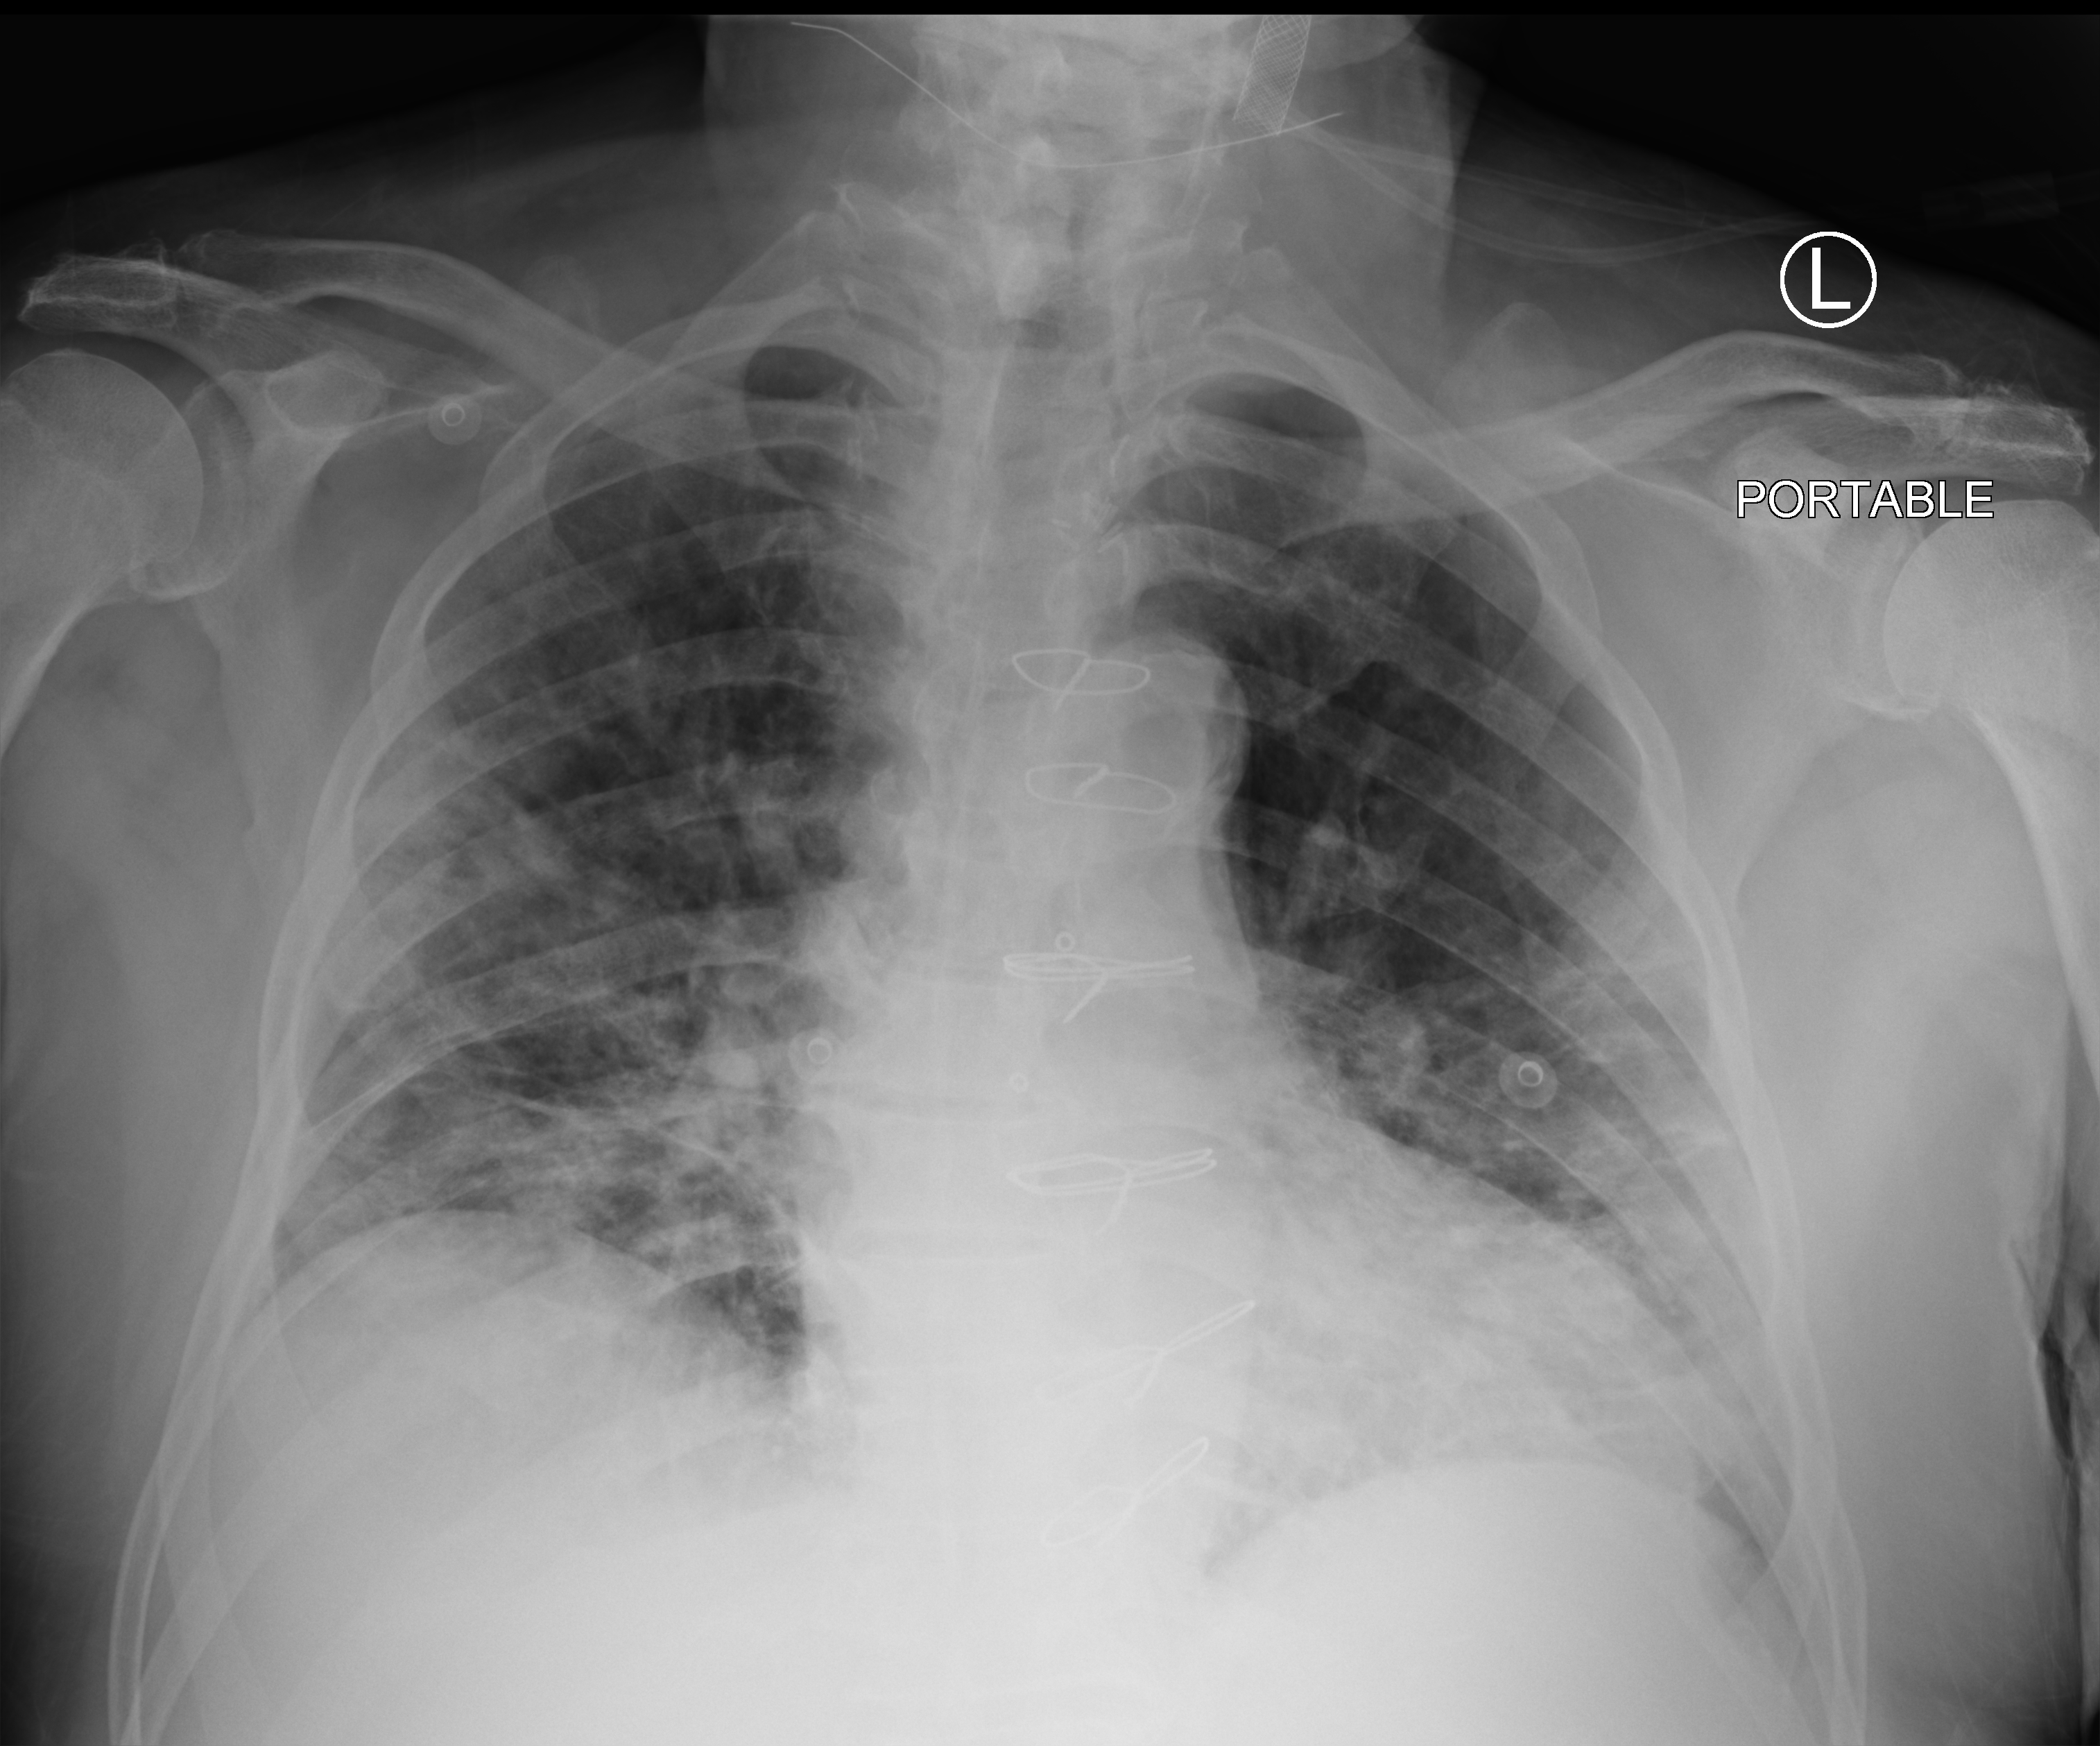
Portable chest radiograph; anteroposterior (AP) projection. Male patient hospitalised with COVID-19, age 75–90 years.
Admission-level facts for this patient (not findings on this image; timing relative to this image not recorded):
- mechanically ventilated during this hospital stay: no
- COPD (admission record): no
- admitted to intensive care during this hospital stay: no